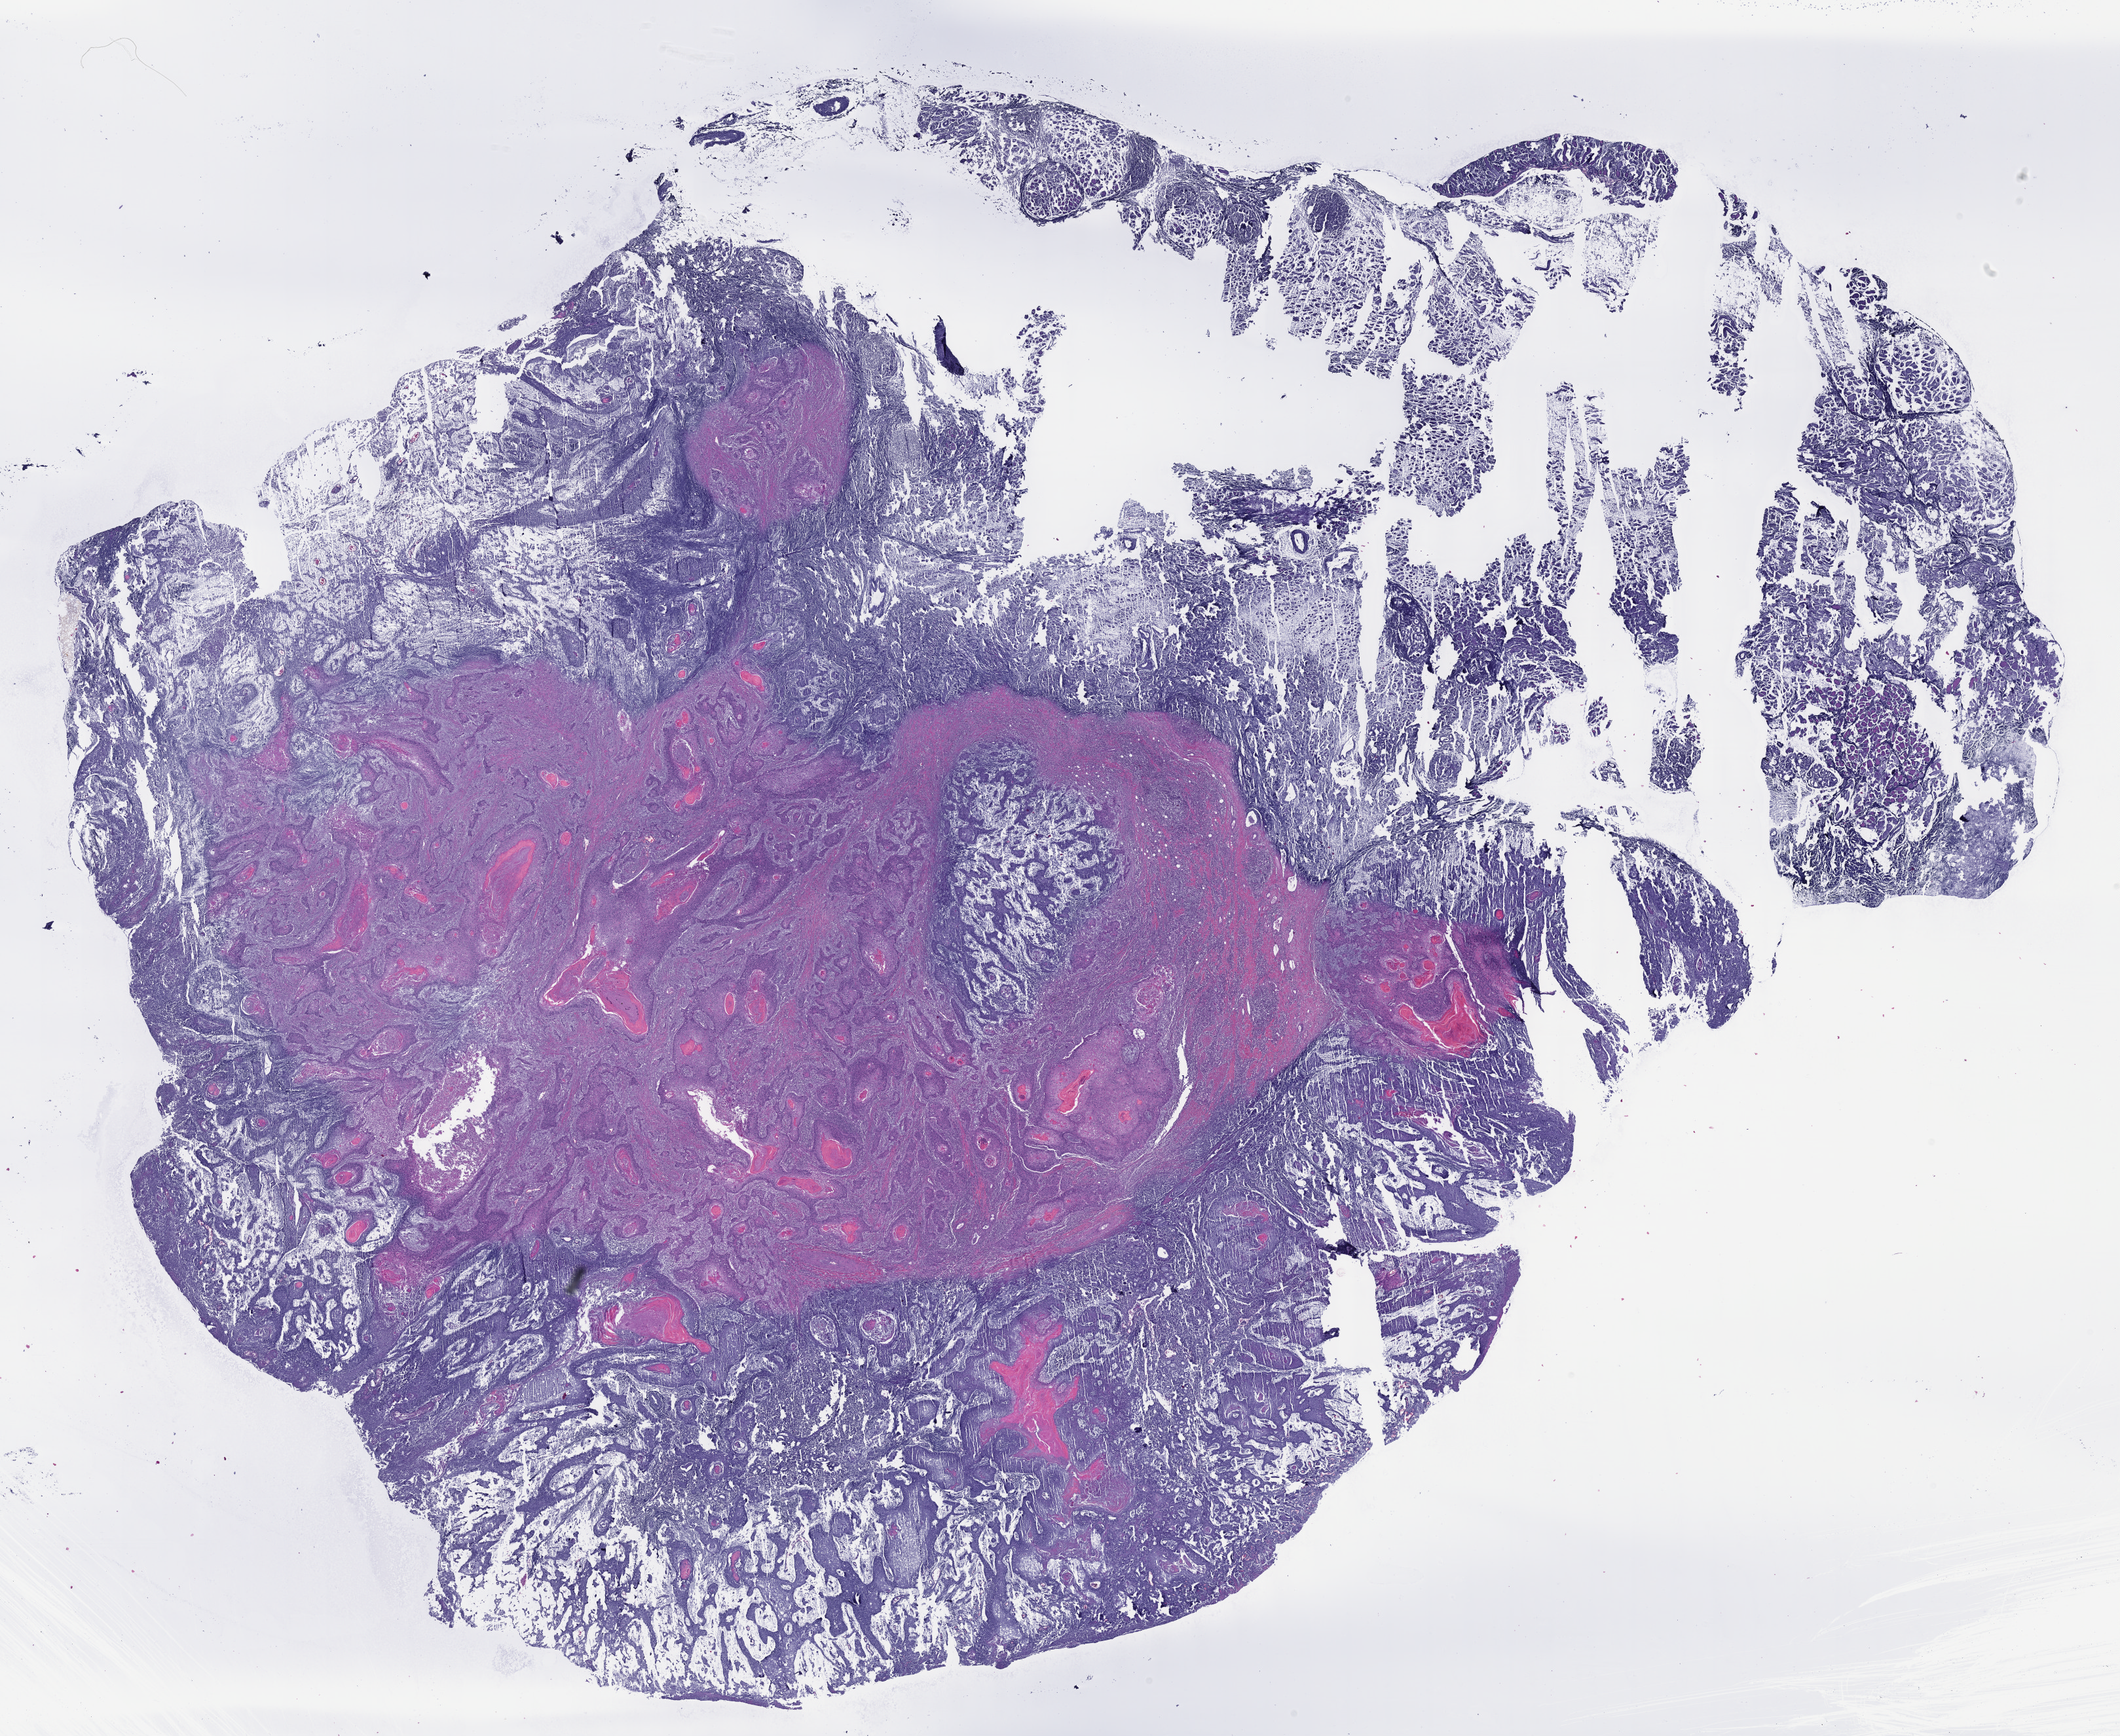
Whole-slide histology image, H&E, a low-resolution overview of the entire scanned area, about 26.2 x 21.4 mm, FFPE section, sample: primary tumour, head and neck. Male, age 68 years at initial diagnosis. Histologic grade: G3 (poorly differentiated).
TNM: T3 N0. AJCC pathologic stage: III. Lymph nodes positive (case pathology): 0 of 65 examined. Pathologic diagnosis: Squamous cell carcinoma, NOS (larynx, NOS).